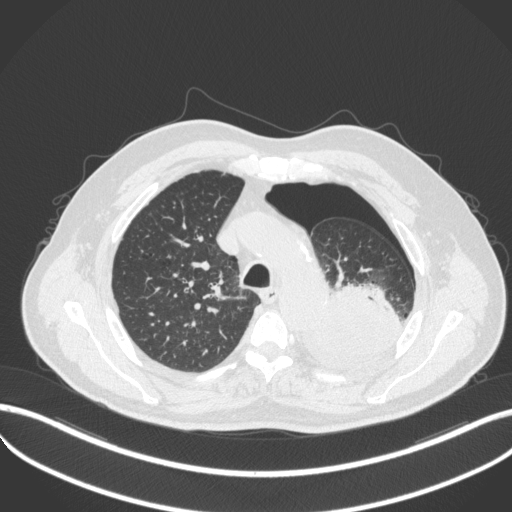
Chest CT, one axial slice; slice 380 of 466 in the series (ordered by position); reconstruction kernel B31f; 120 kVp; lung window (W 1500 / L -600 HU); 1 mm slice thickness; 512 × 512 image matrix, field of view 400 × 400 mm. Patient: male, 76 years. Case-level facts recorded for this patient, not image findings: clinical TNM (as recorded): T3 N0 M1b.
Annotated regions visible in this slice (rectangle marked by the reading radiologist):
- lung tumour (recorded histology: adenocarcinoma): box from (x=296, y=277) to (x=405, y=377) px